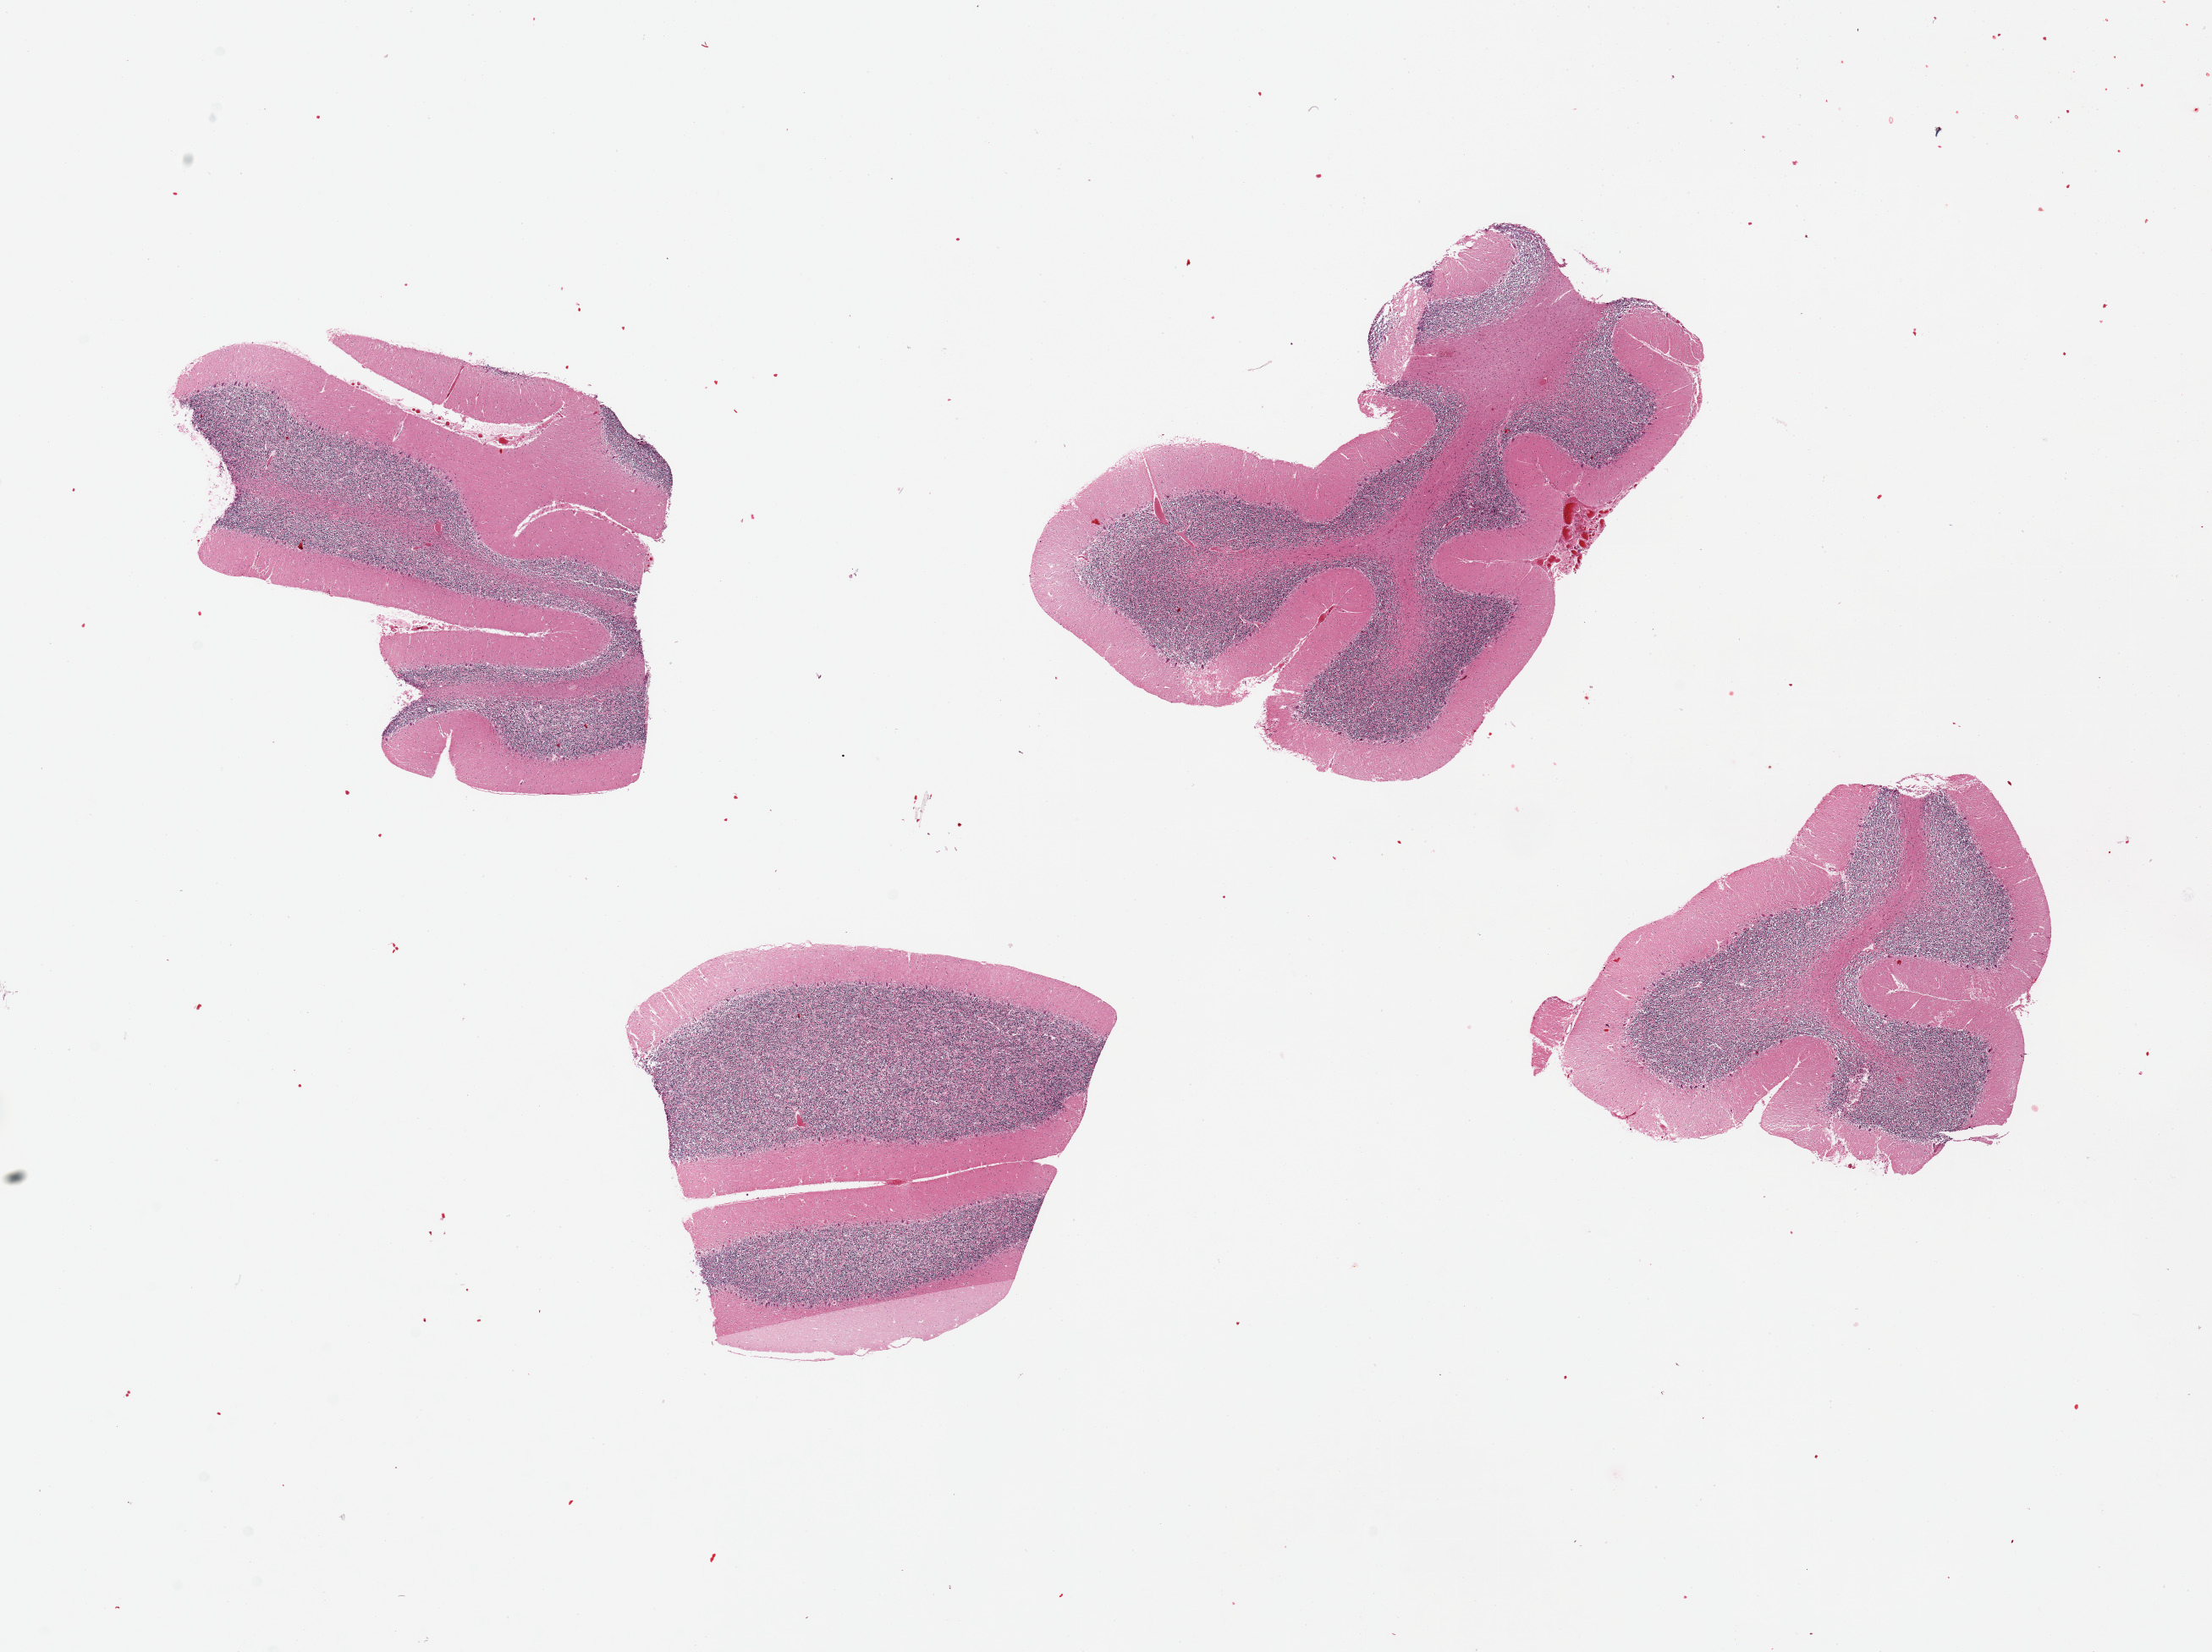
Whole-slide image, hematoxylin and eosin (H&E) stain, brightfield — whole scanned area (about 20.7 x 15.4 mm, slide scanned at 20x) shown as a low-resolution overview. PAXgene-fixed paraffin-embedded (PFPE) section. Sampled site (target tissue): cerebellum. Tissue donor sample. Male donor.
Pathologist's review note for this sample: 4 pieces.